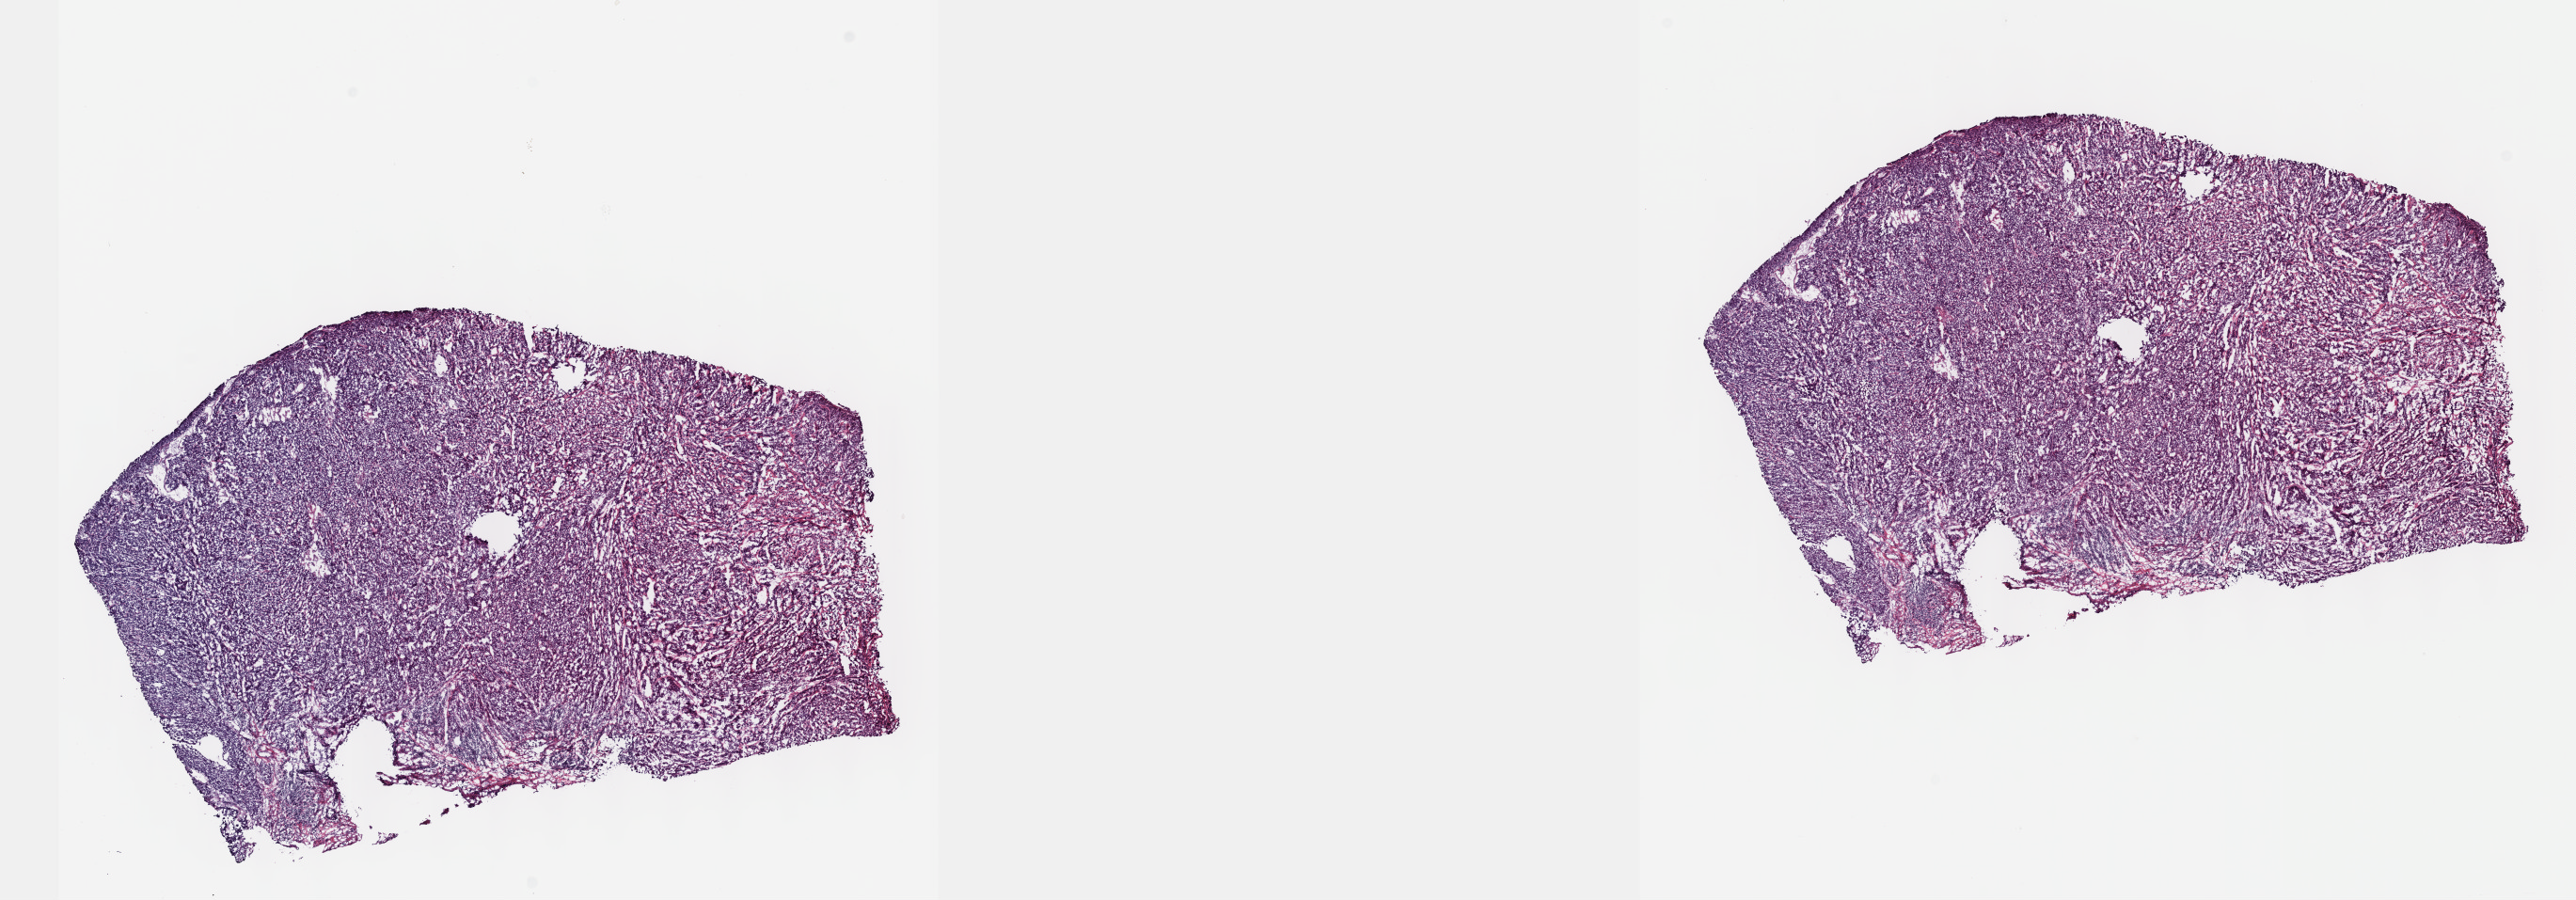
Whole-slide histology image, Hematoxylin and eosin (H&E) stained — low-resolution overview of the scanned area, about 22.1 x 7.7 mm; frozen section from the top of the tissue portion; cervix, primary tumour sample. Female patient; age at initial diagnosis 41 years. Histologic grade: G3 (poorly differentiated). Slide review estimates, as recorded: tumour cells 90%, tumour nuclei 90%, normal cells 0%, stromal cells 10%, necrosis 0%. Infiltration values recorded for this section: lymphocyte infiltration 40%, monocyte infiltration 20%, neutrophil infiltration 20%.
* FIGO stage: IB2
* histologic diagnosis: Adenosquamous carcinoma